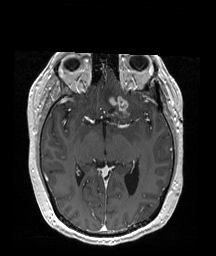
Brain MRI from a brain-tumour surgery series, one axial slice; slice 106 of 192 in the series (ordered by position); T1-weighted post-contrast; 1 mm slice thickness; 216 × 256 image matrix, field of view 211 × 250 mm. Case-level facts recorded for this patient, not image findings: histopathology: Oligodendroglioma; WHO grade: 2; IDH mutation: yes.
Annotated regions visible in this slice (outlined manually by an expert reader):
- tumour: box from (x=107, y=95) to (x=132, y=117) px